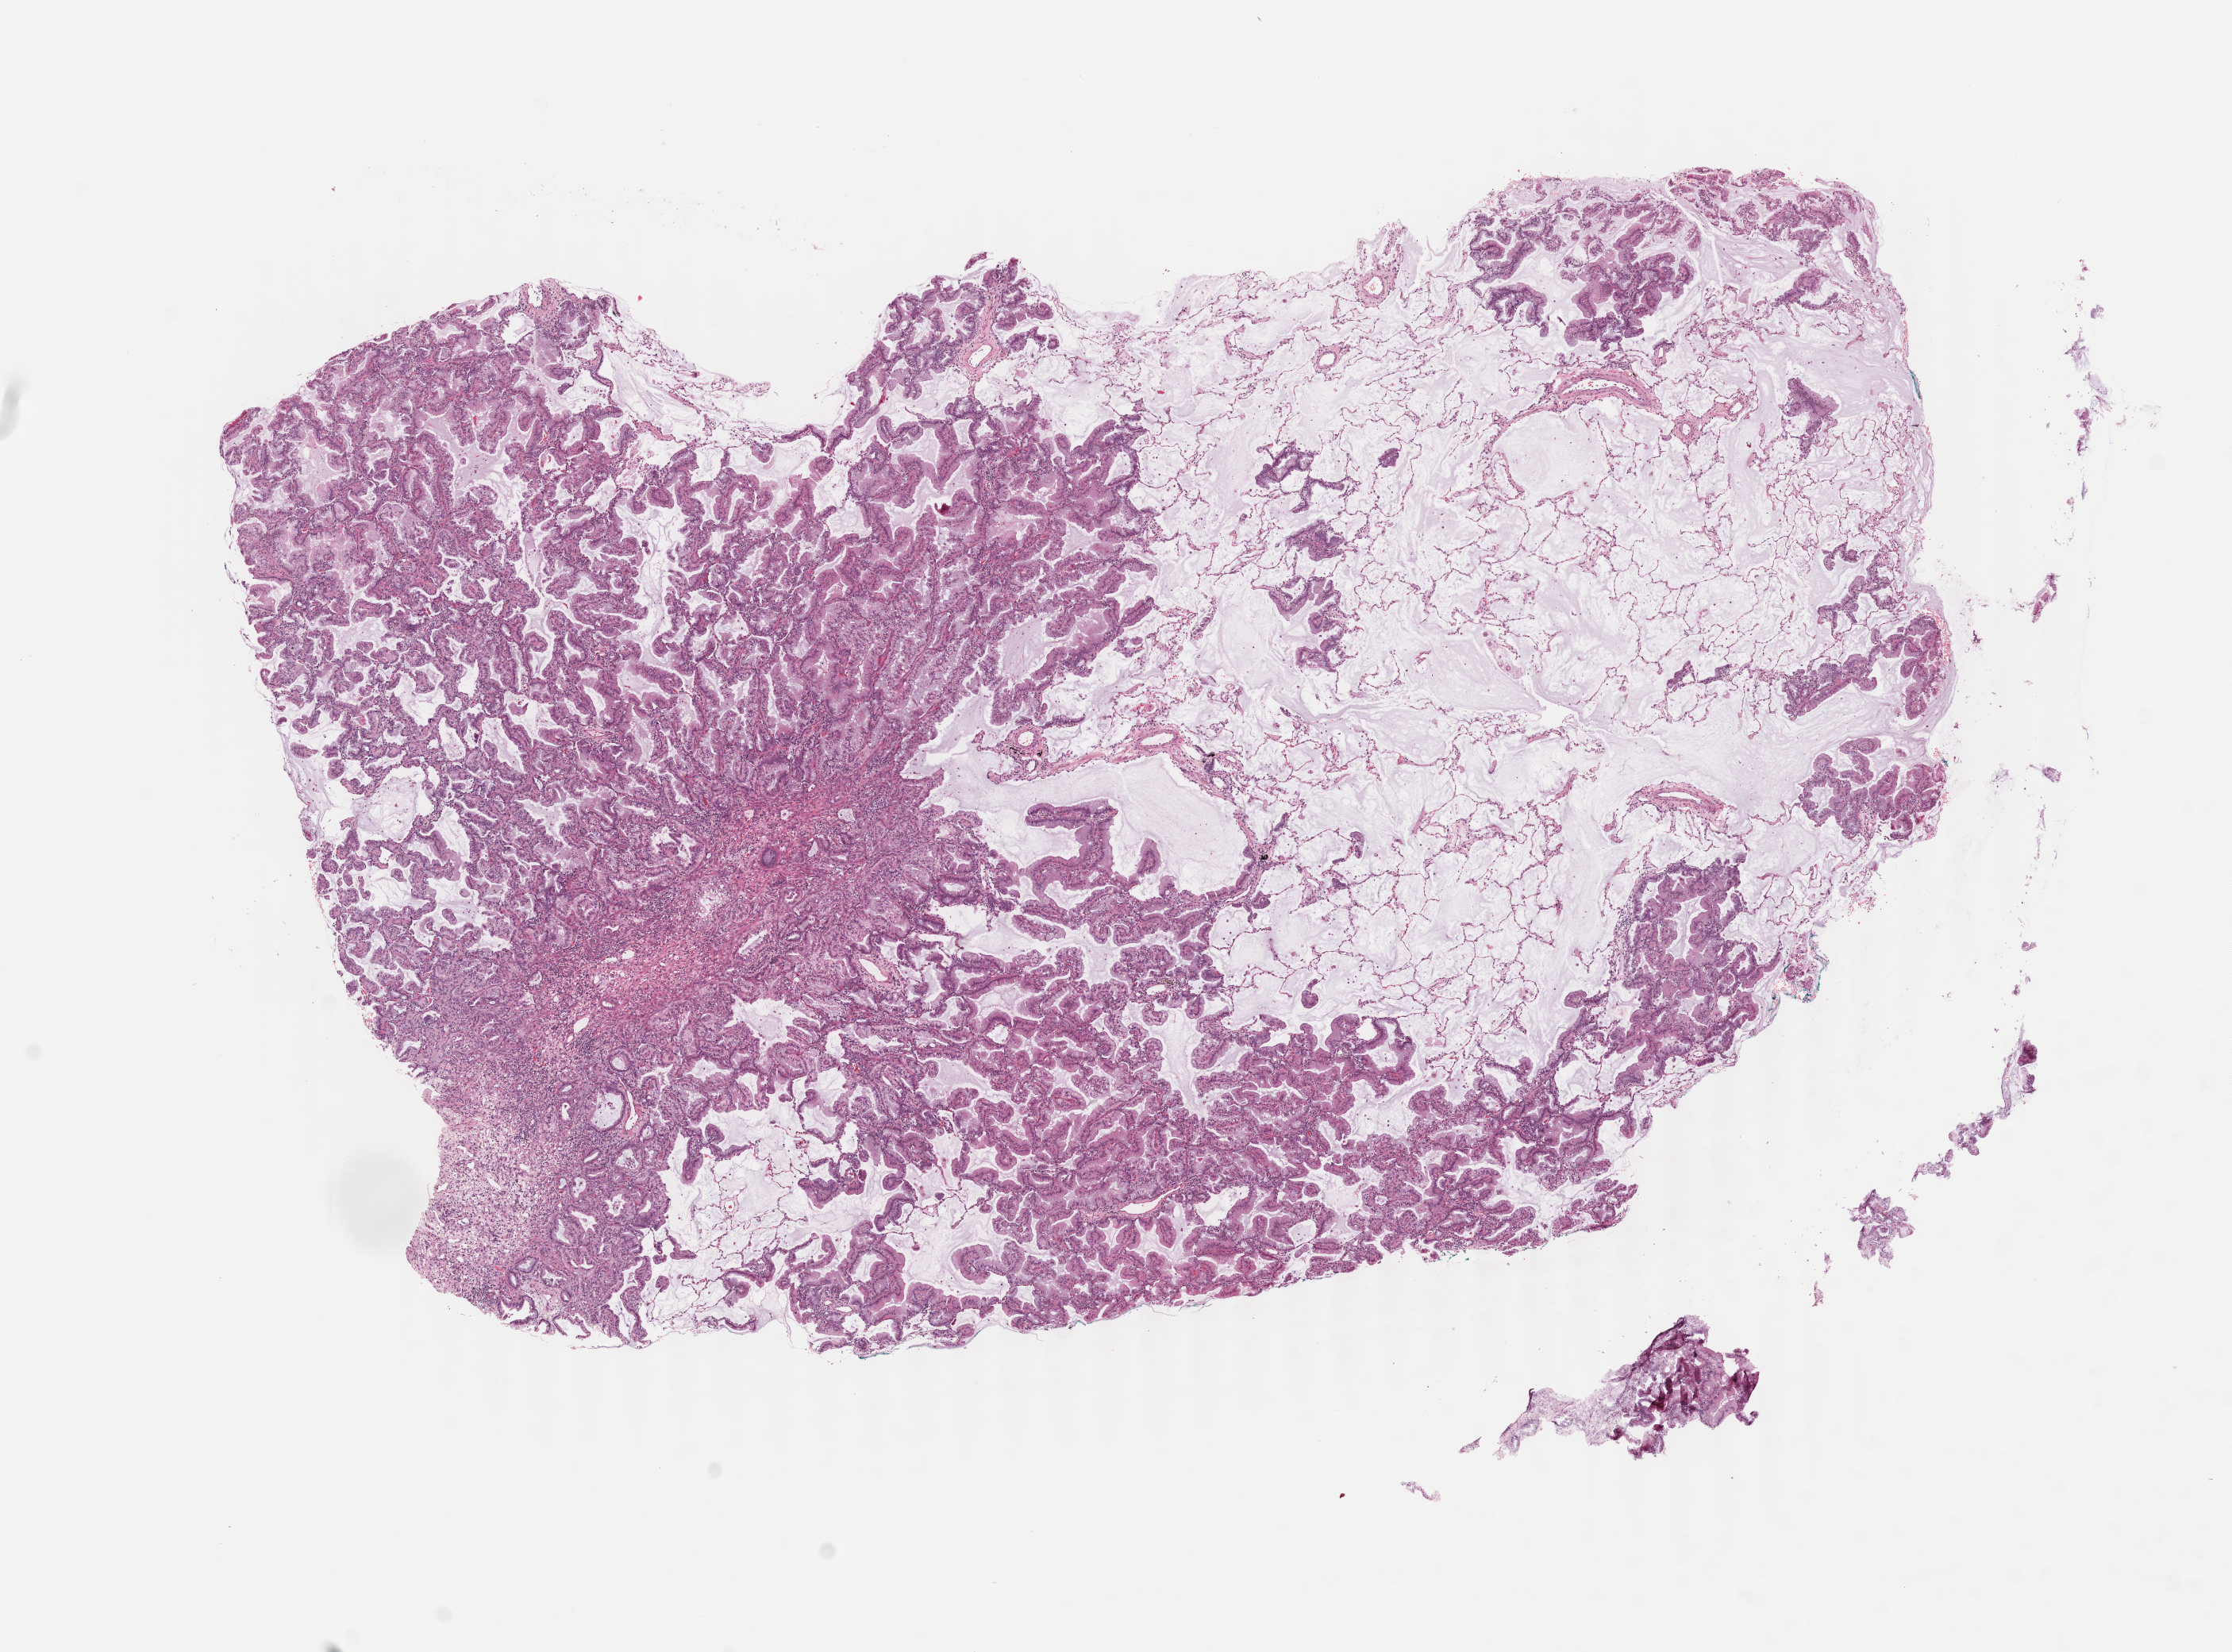
Digitized Hematoxylin and eosin (H&E) stained tissue section (whole slide), low-resolution overview of the scanned area, about 11.2 x 8.3 mm; frozen section; lung, primary tumour sample. Patient: male, age at initial diagnosis 64 years. Composition of this section per pathologist review: tumour cells 79%, tumour nuclei 80%.
Diagnosis: Mucinous adenocarcinoma (lower lobe, lung).